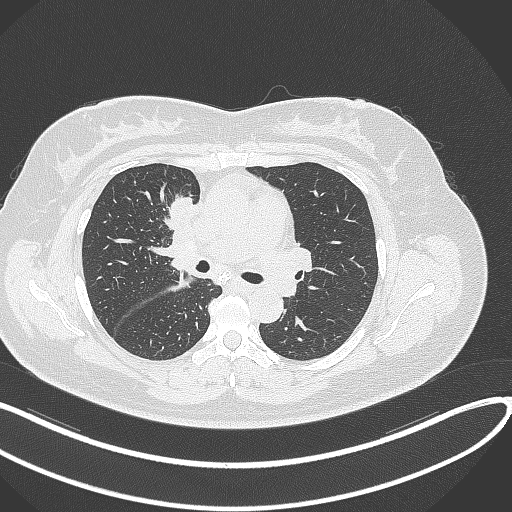
Chest CT, one axial slice; 120 kVp; lung window (W 1500 / L -600 HU); 1 mm slice thickness; 512 × 512 image matrix. Female patient, age 46 years. Case-level facts recorded for this patient, not image findings: clinical TNM (as recorded): T2a N1 M0.
Structures marked on this image (rectangle marked by the reading radiologist):
- lung tumour (recorded histology: adenocarcinoma): bounding box <167,193,202,238> (left, top, right, bottom; pixels)